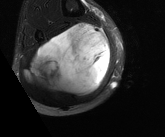
MRI of an extremity soft-tissue mass, one axial slice. Slice 70 of 81 in the series (ordered by position). T2-weighted fat-saturated. MR volume resampled by the dataset authors to the PET/CT grid (not the native acquisition matrix). 3.27 mm slice thickness. 165 × 137 image matrix. Male patient. From the clinical record (not read from this slice): histological type: liposarcoma - round cell; grade: high; site of the primary tumour: right calf.
Structures marked on this image (expert contour drawn on MRI and transferred to this co-registered scan by the dataset authors):
- gross tumour volume (mass): box from (x=25, y=23) to (x=111, y=97) px